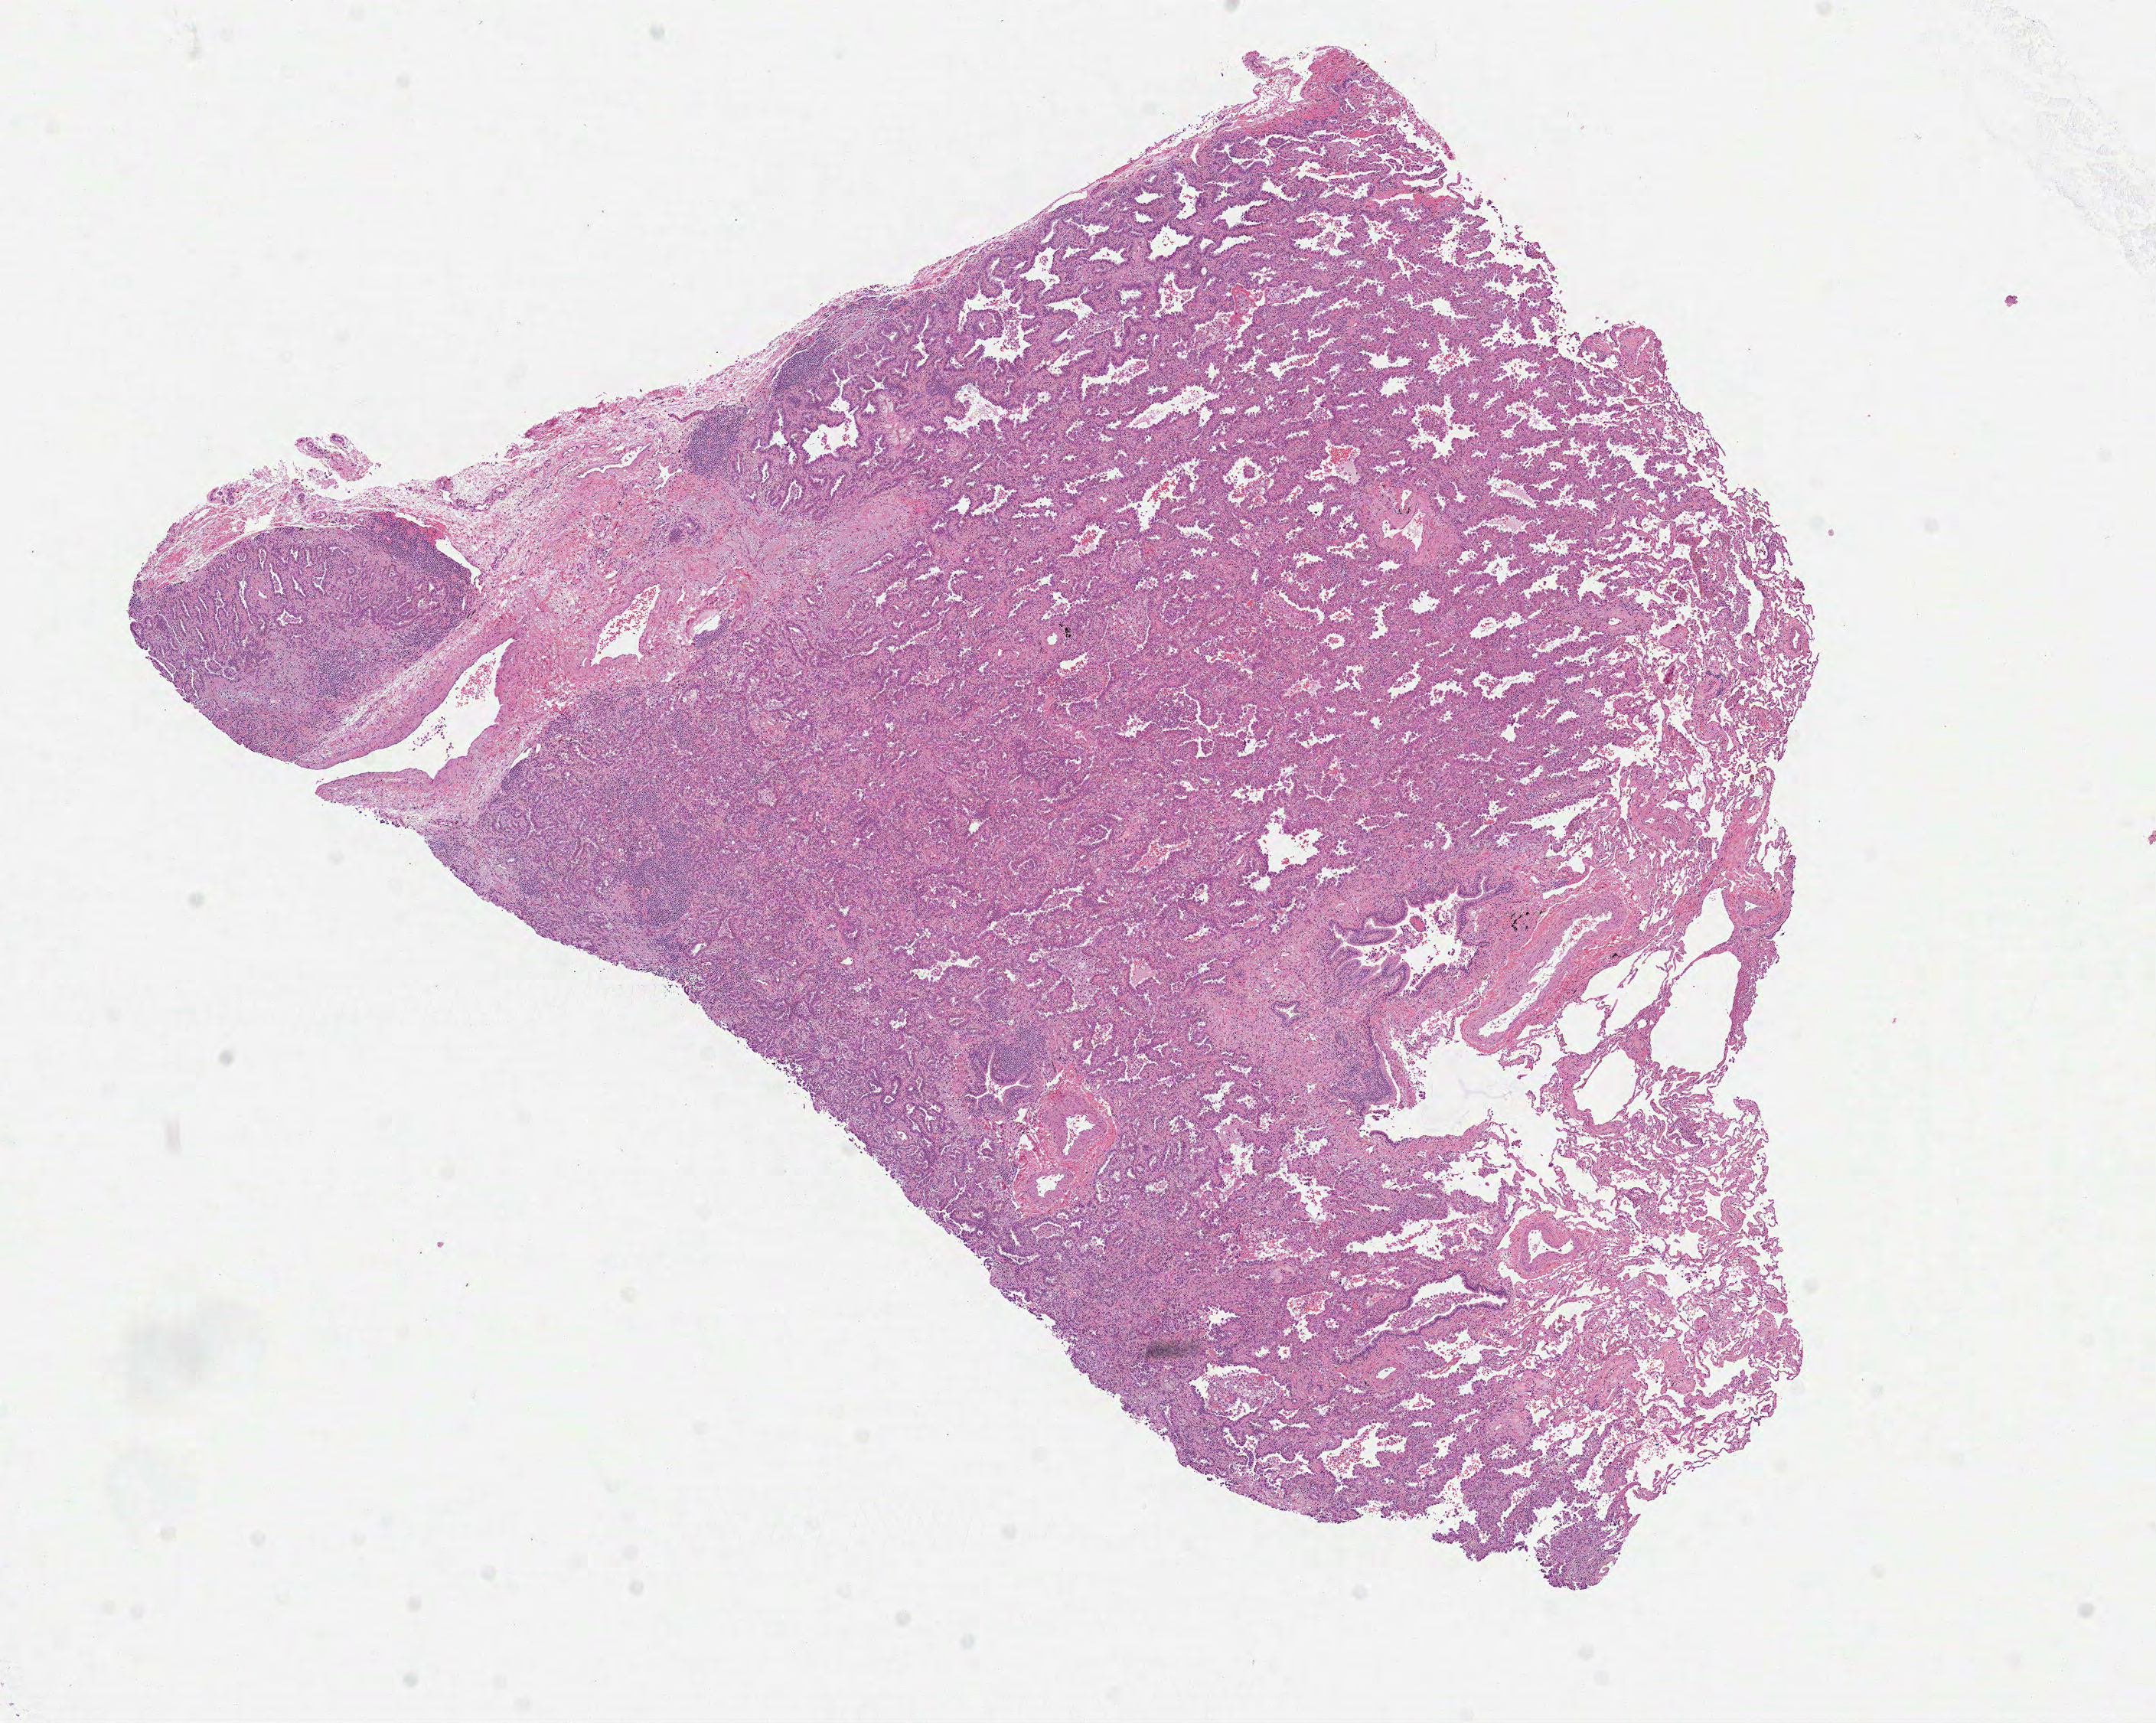
H&E-stained whole-slide image, low-resolution overview of the scanned area, about 11.4 x 9.1 mm (from a 40x scan); formalin-fixed paraffin-embedded (FFPE) diagnostic section; sample: primary tumour, lung. Patient: female, age at initial diagnosis 72 years.
Histologic diagnosis: Adenocarcinoma, NOS. AJCC pathologic stage: IA (7th edition). Laterality: right. TNM: T1b N0 MX.